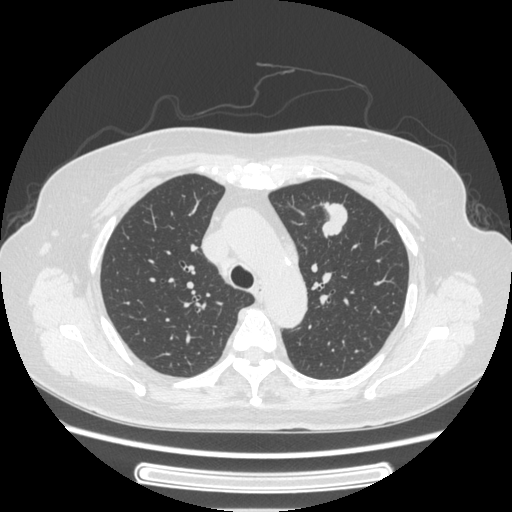
Chest CT, one axial slice. 120 kVp. Lung window (W 1500 / L -600 HU). 1.25 mm slice thickness. 512 × 512 image matrix, field of view 363 × 363 mm. Female patient, age 77 years. From the clinical record (not read from this slice): clinical TNM (as recorded): T1c N3 M0.
Structures marked on this image (rectangle marked by the reading radiologist):
- lung tumour (recorded histology: adenocarcinoma): bounding box [x1, y1, x2, y2] px = [312, 192, 351, 240]